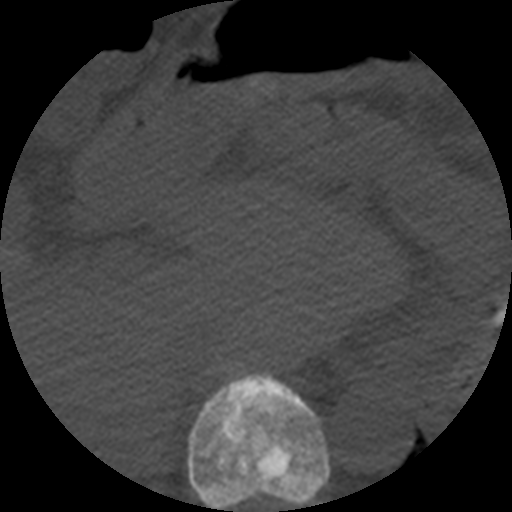
CT including the spine, one axial slice. Bone window (W 1800 / L 400 HU). 1.25 mm slice thickness. 512 × 512 image matrix, field of view 160 × 160 mm. Patient age 57 years. Case-level facts recorded for this patient, not image findings: primary cancer: prostate.
Structures marked on this image (semi-automatic segmentation, software-assisted and operator-edited):
- T10 vertebra: bounding box [x1, y1, x2, y2] px = [188, 373, 330, 512]